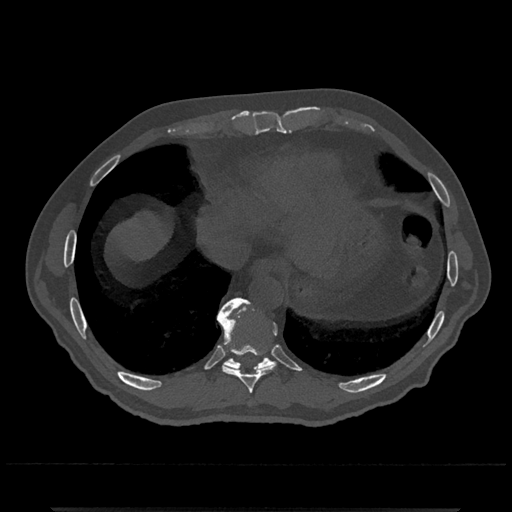
CT including the spine, one axial slice; position 591 of 797 along the scan axis; bone window (W 1800 / L 400 HU); 0.5 mm slice thickness; 512 × 512 image matrix, field of view 393 × 393 mm. Male patient, age 67 years. From the clinical record (not read from this slice): primary cancer: prostate.
Structures marked on this image (semi-automatically segmented with operator editing):
- T10 vertebra: bounding box [x1, y1, x2, y2] px = [218, 298, 276, 371]
- T9 vertebra: [217, 301, 278, 394]